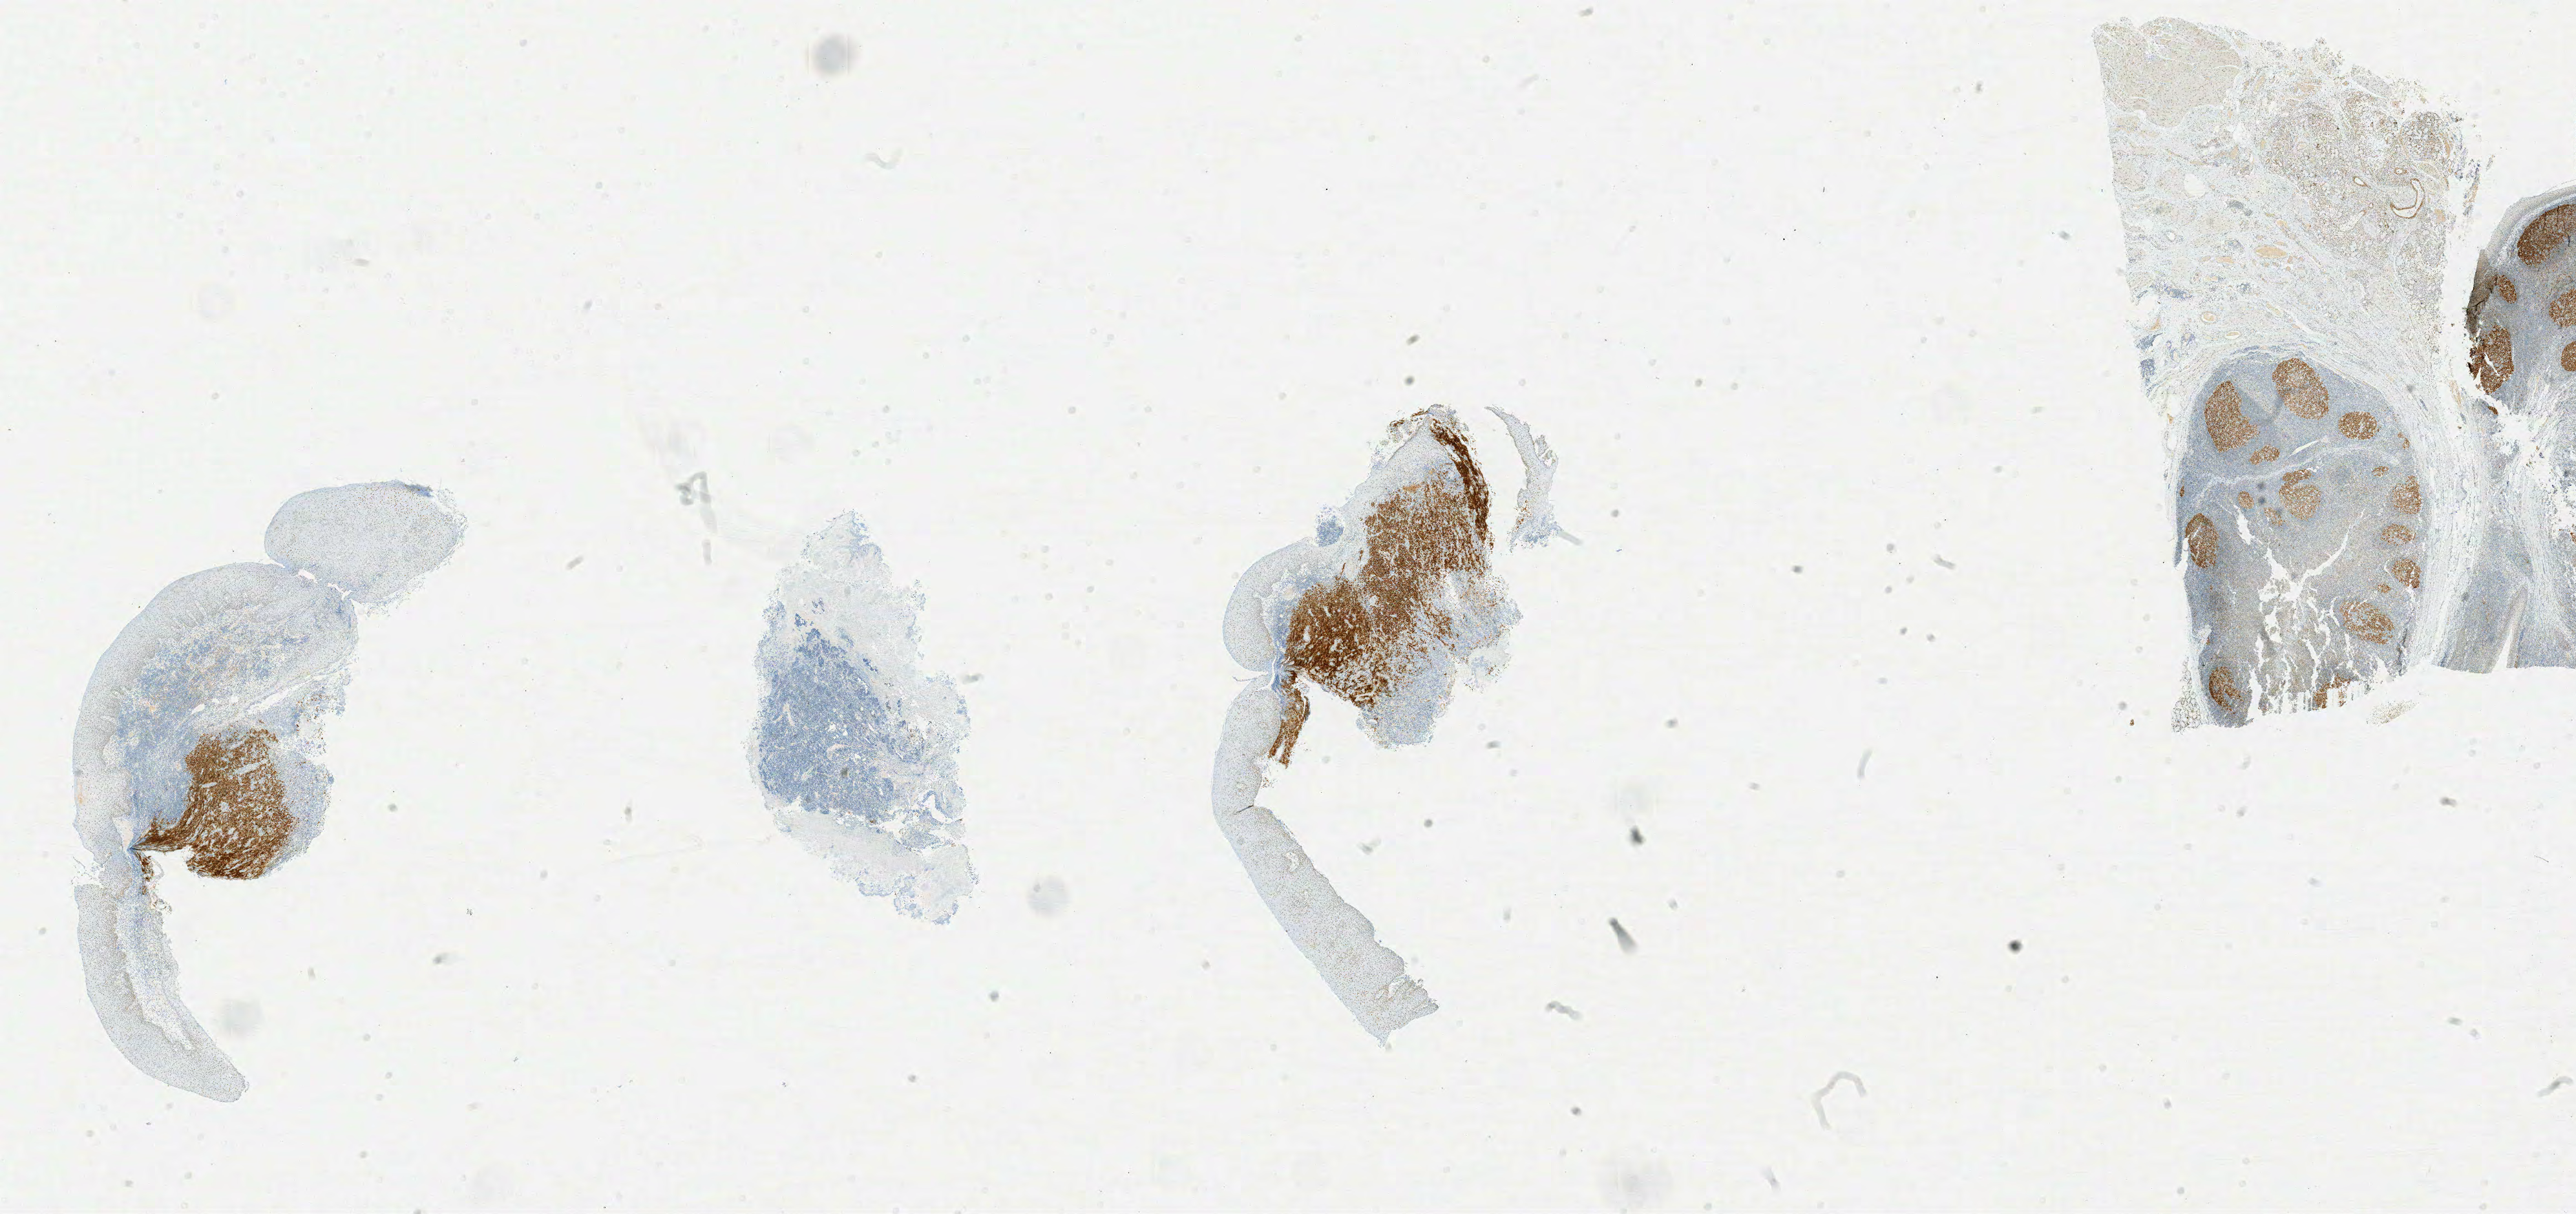
Whole-slide image, immunohistochemical stain for BCL6 — a low-resolution overview of the entire scanned area, about 31.8 x 15.0 mm, specimen: tumor tissue. Patient: male, age 66 years.
Histologic diagnosis: Burkitt lymphoma, NOS.